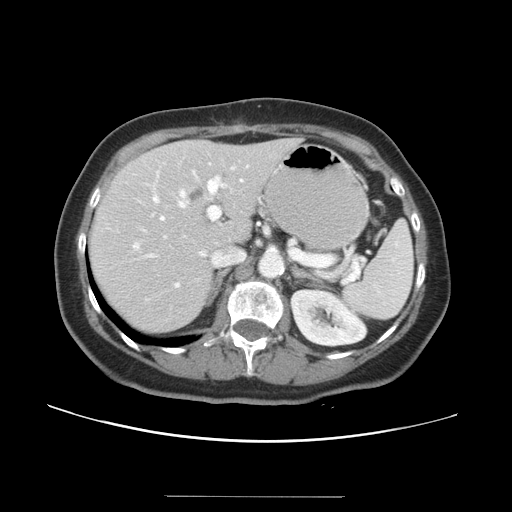
Contrast-enhanced abdominal CT, one axial slice. Slice 22 of 34 in the series (ordered by position). Reconstruction kernel STANDARD. 120 kVp. Intravenous contrast given. Soft-tissue window (W 400 / L 40 HU). 5 mm slice thickness. 512 × 512 image matrix, field of view 382 × 382 mm. Female patient, age 69 years. Case-level facts recorded for this patient, not image findings: diagnosis: colorectal cancer liver metastases, imaged before liver resection; multiple liver metastases: yes; largest metastasis: 1.4 cm; chemotherapy before resection: no.
Annotated regions visible in this slice (outlined manually by an expert reader):
- hepatic veins: bounding box <175,166,248,288> (left, top, right, bottom; pixels)
- liver: <90,139,299,333>
- planned liver remnant (the part of the liver to remain after resection): <90,139,299,333>
- portal vein (with intrahepatic branches): <133,177,360,282>
- liver metastasis: <187,185,206,204>